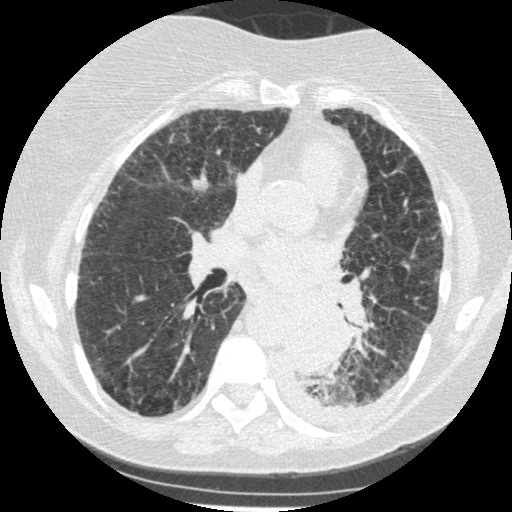
Low-dose screening chest CT, one axial slice; position 126 of 341 along the scan axis; 120 kVp; lung window (W 1500 / L -600 HU); 512 × 512 image matrix.
Structures marked on this image (expert manual segmentation):
- lesion 1 (tumor, lower lobe of left lung): bounding box (x1, y1, x2, y2) in pixels: (284, 302, 346, 375)